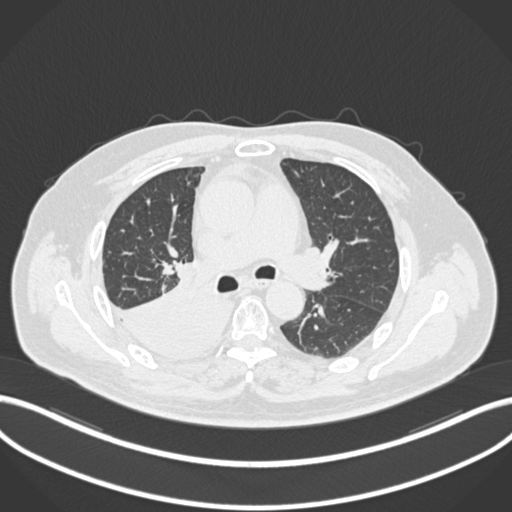
Chest CT, one axial slice; reconstruction kernel B30f; lung window (W 1500 / L -600 HU); 512 × 512 image matrix, field of view 400 × 400 mm. Patient: male, 68 years. Case-level facts recorded for this patient, not image findings: clinical TNM (as recorded): T2a N0 M0.
Annotated regions visible in this slice (bounding box drawn by a radiologist):
- lung tumour (recorded histology: adenocarcinoma): bounding box [x1, y1, x2, y2] px = [108, 287, 234, 357]